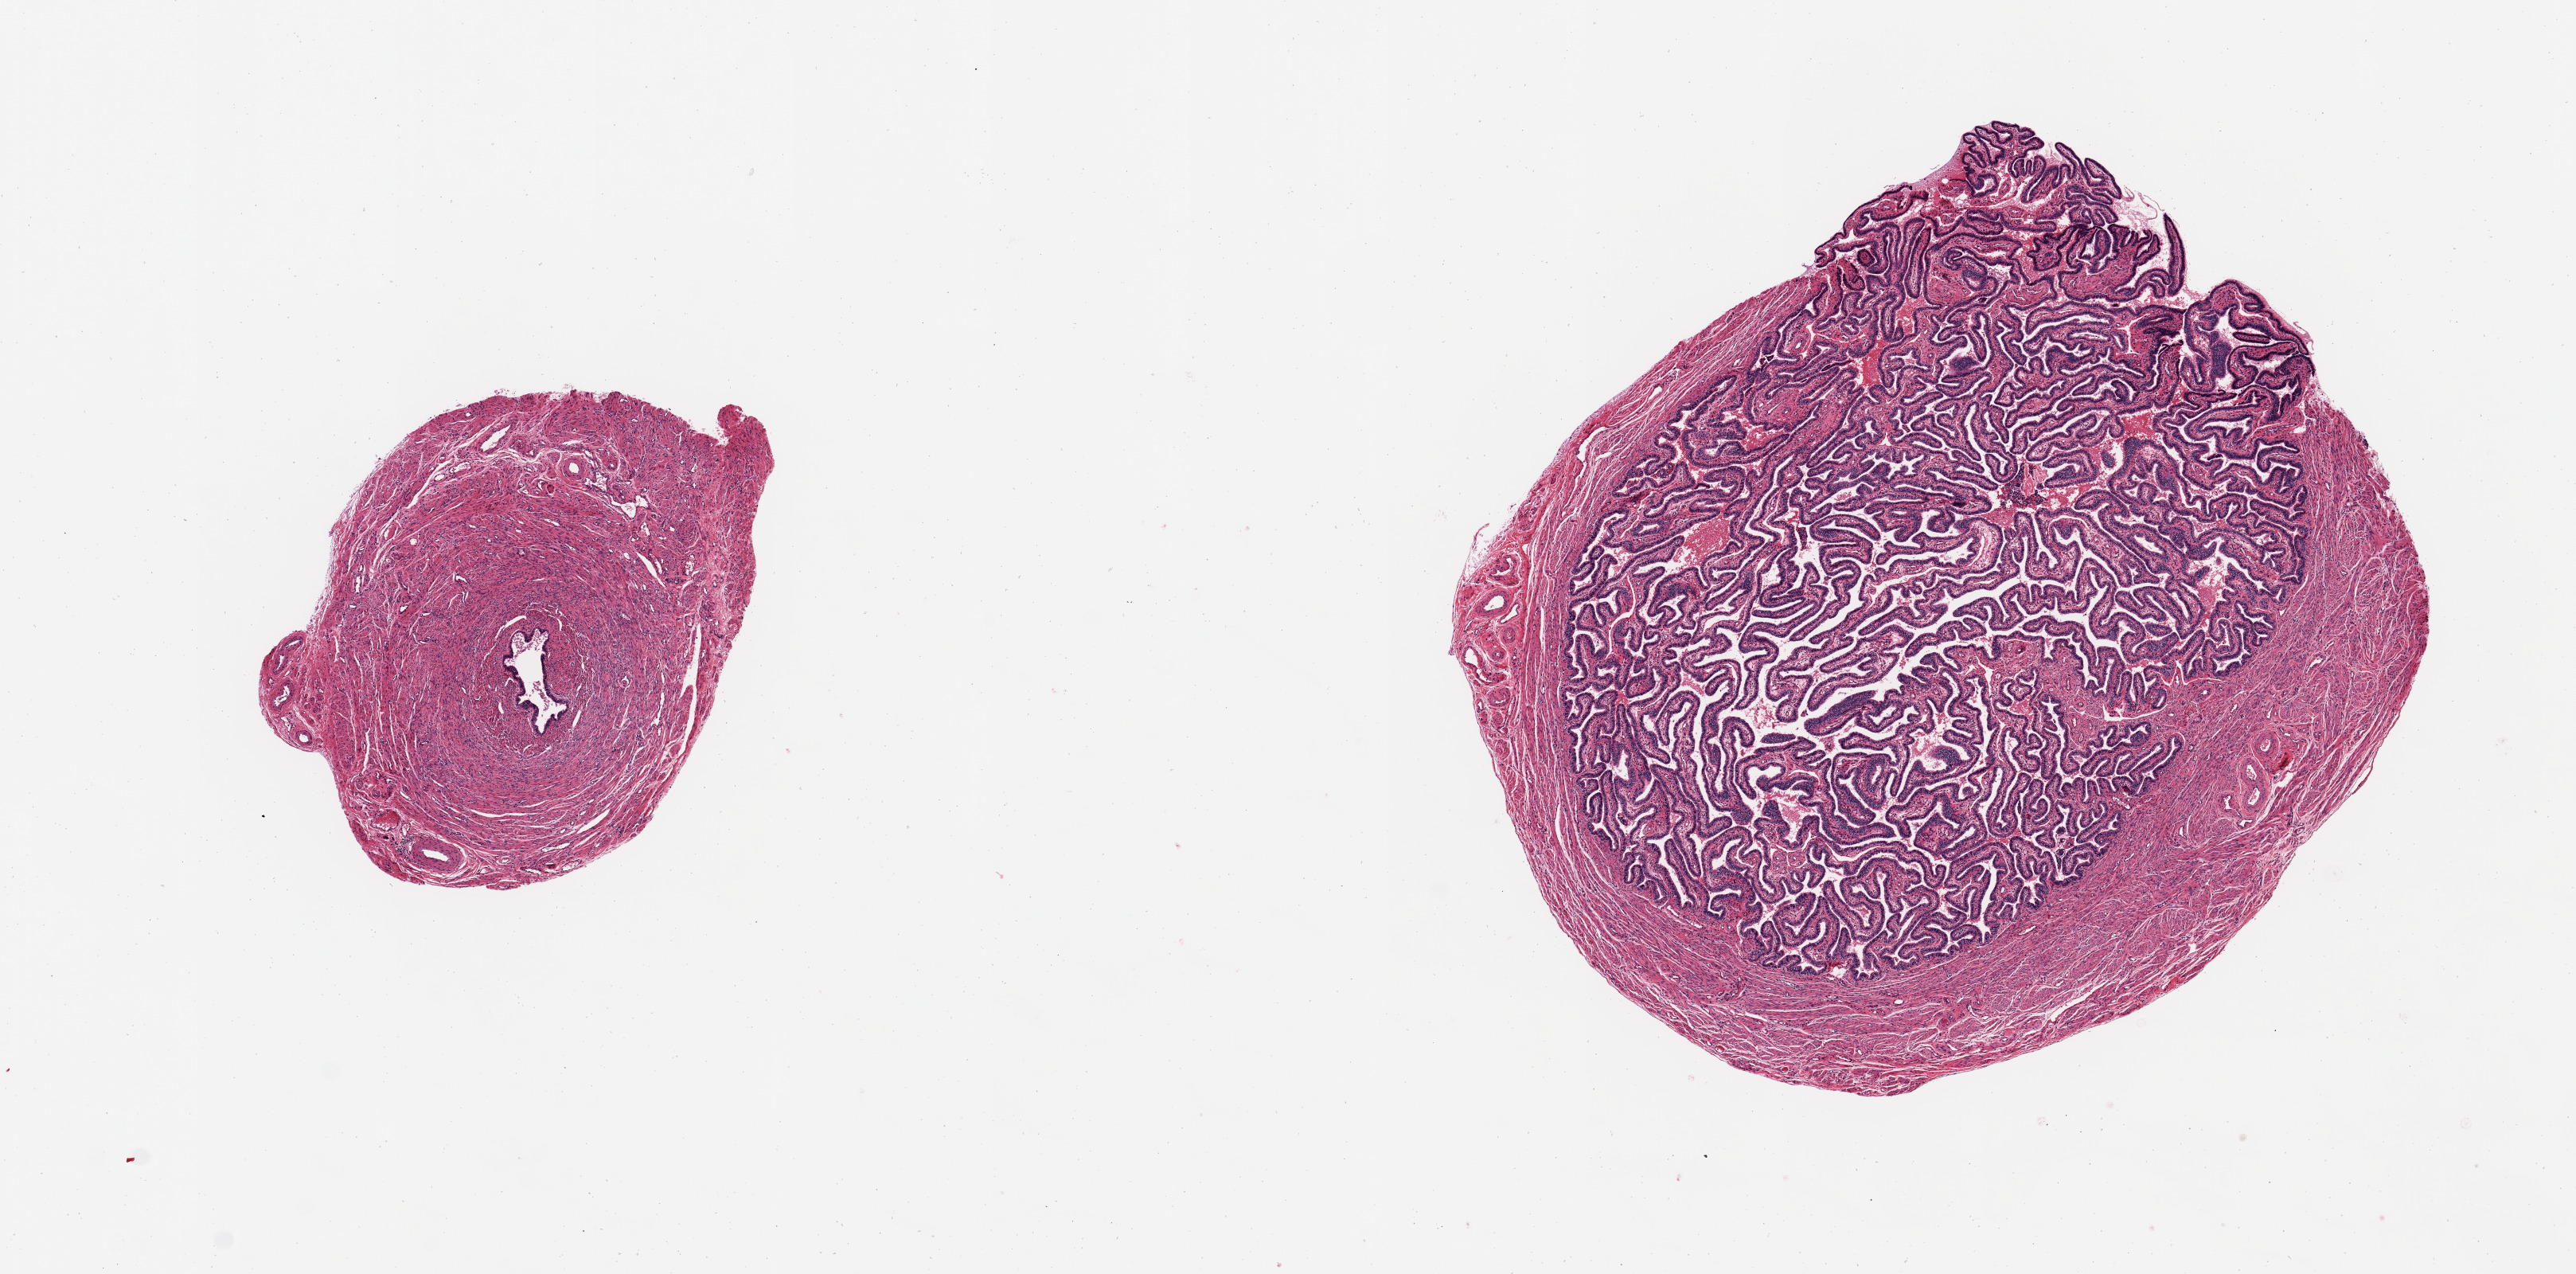
Digitized hematoxylin and eosin (H&E)-stained section — whole scanned area (about 12.8 x 6.3 mm, acquisition: 20x scan) shown as a low-resolution overview; PAXgene-fixed paraffin-embedded (PFPE) section; section of fallopian tube (target tissue); donor tissue sample. Donor: female.
- reviewer comment on this tissue sample: 2 pieces, 2.6 & 4.5 (ampulla) mm diameter